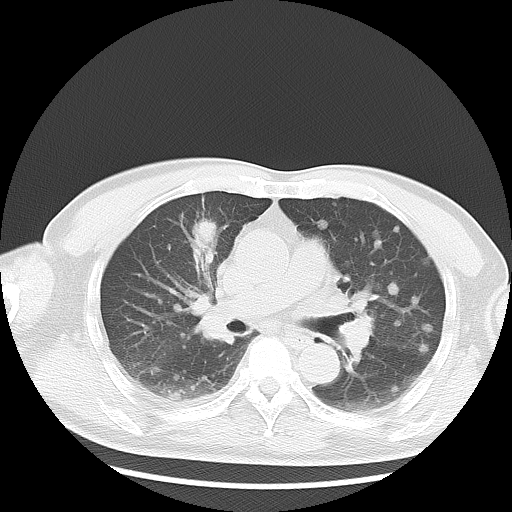
Chest CT, one axial slice. Slice 13 of 35 in the series (ordered by position). Lung window (W 1500 / L -600 HU). 5 mm slice thickness. 512 × 512 image matrix, field of view 369 × 369 mm. Male patient, age 57 years. Case-level facts recorded for this patient, not image findings: clinical TNM (as recorded): T2 N3 M1a.
Structures marked on this image (bounding box drawn by a radiologist):
- lung tumour (recorded histology: adenocarcinoma): bounding box [x1, y1, x2, y2] px = [184, 214, 216, 254]